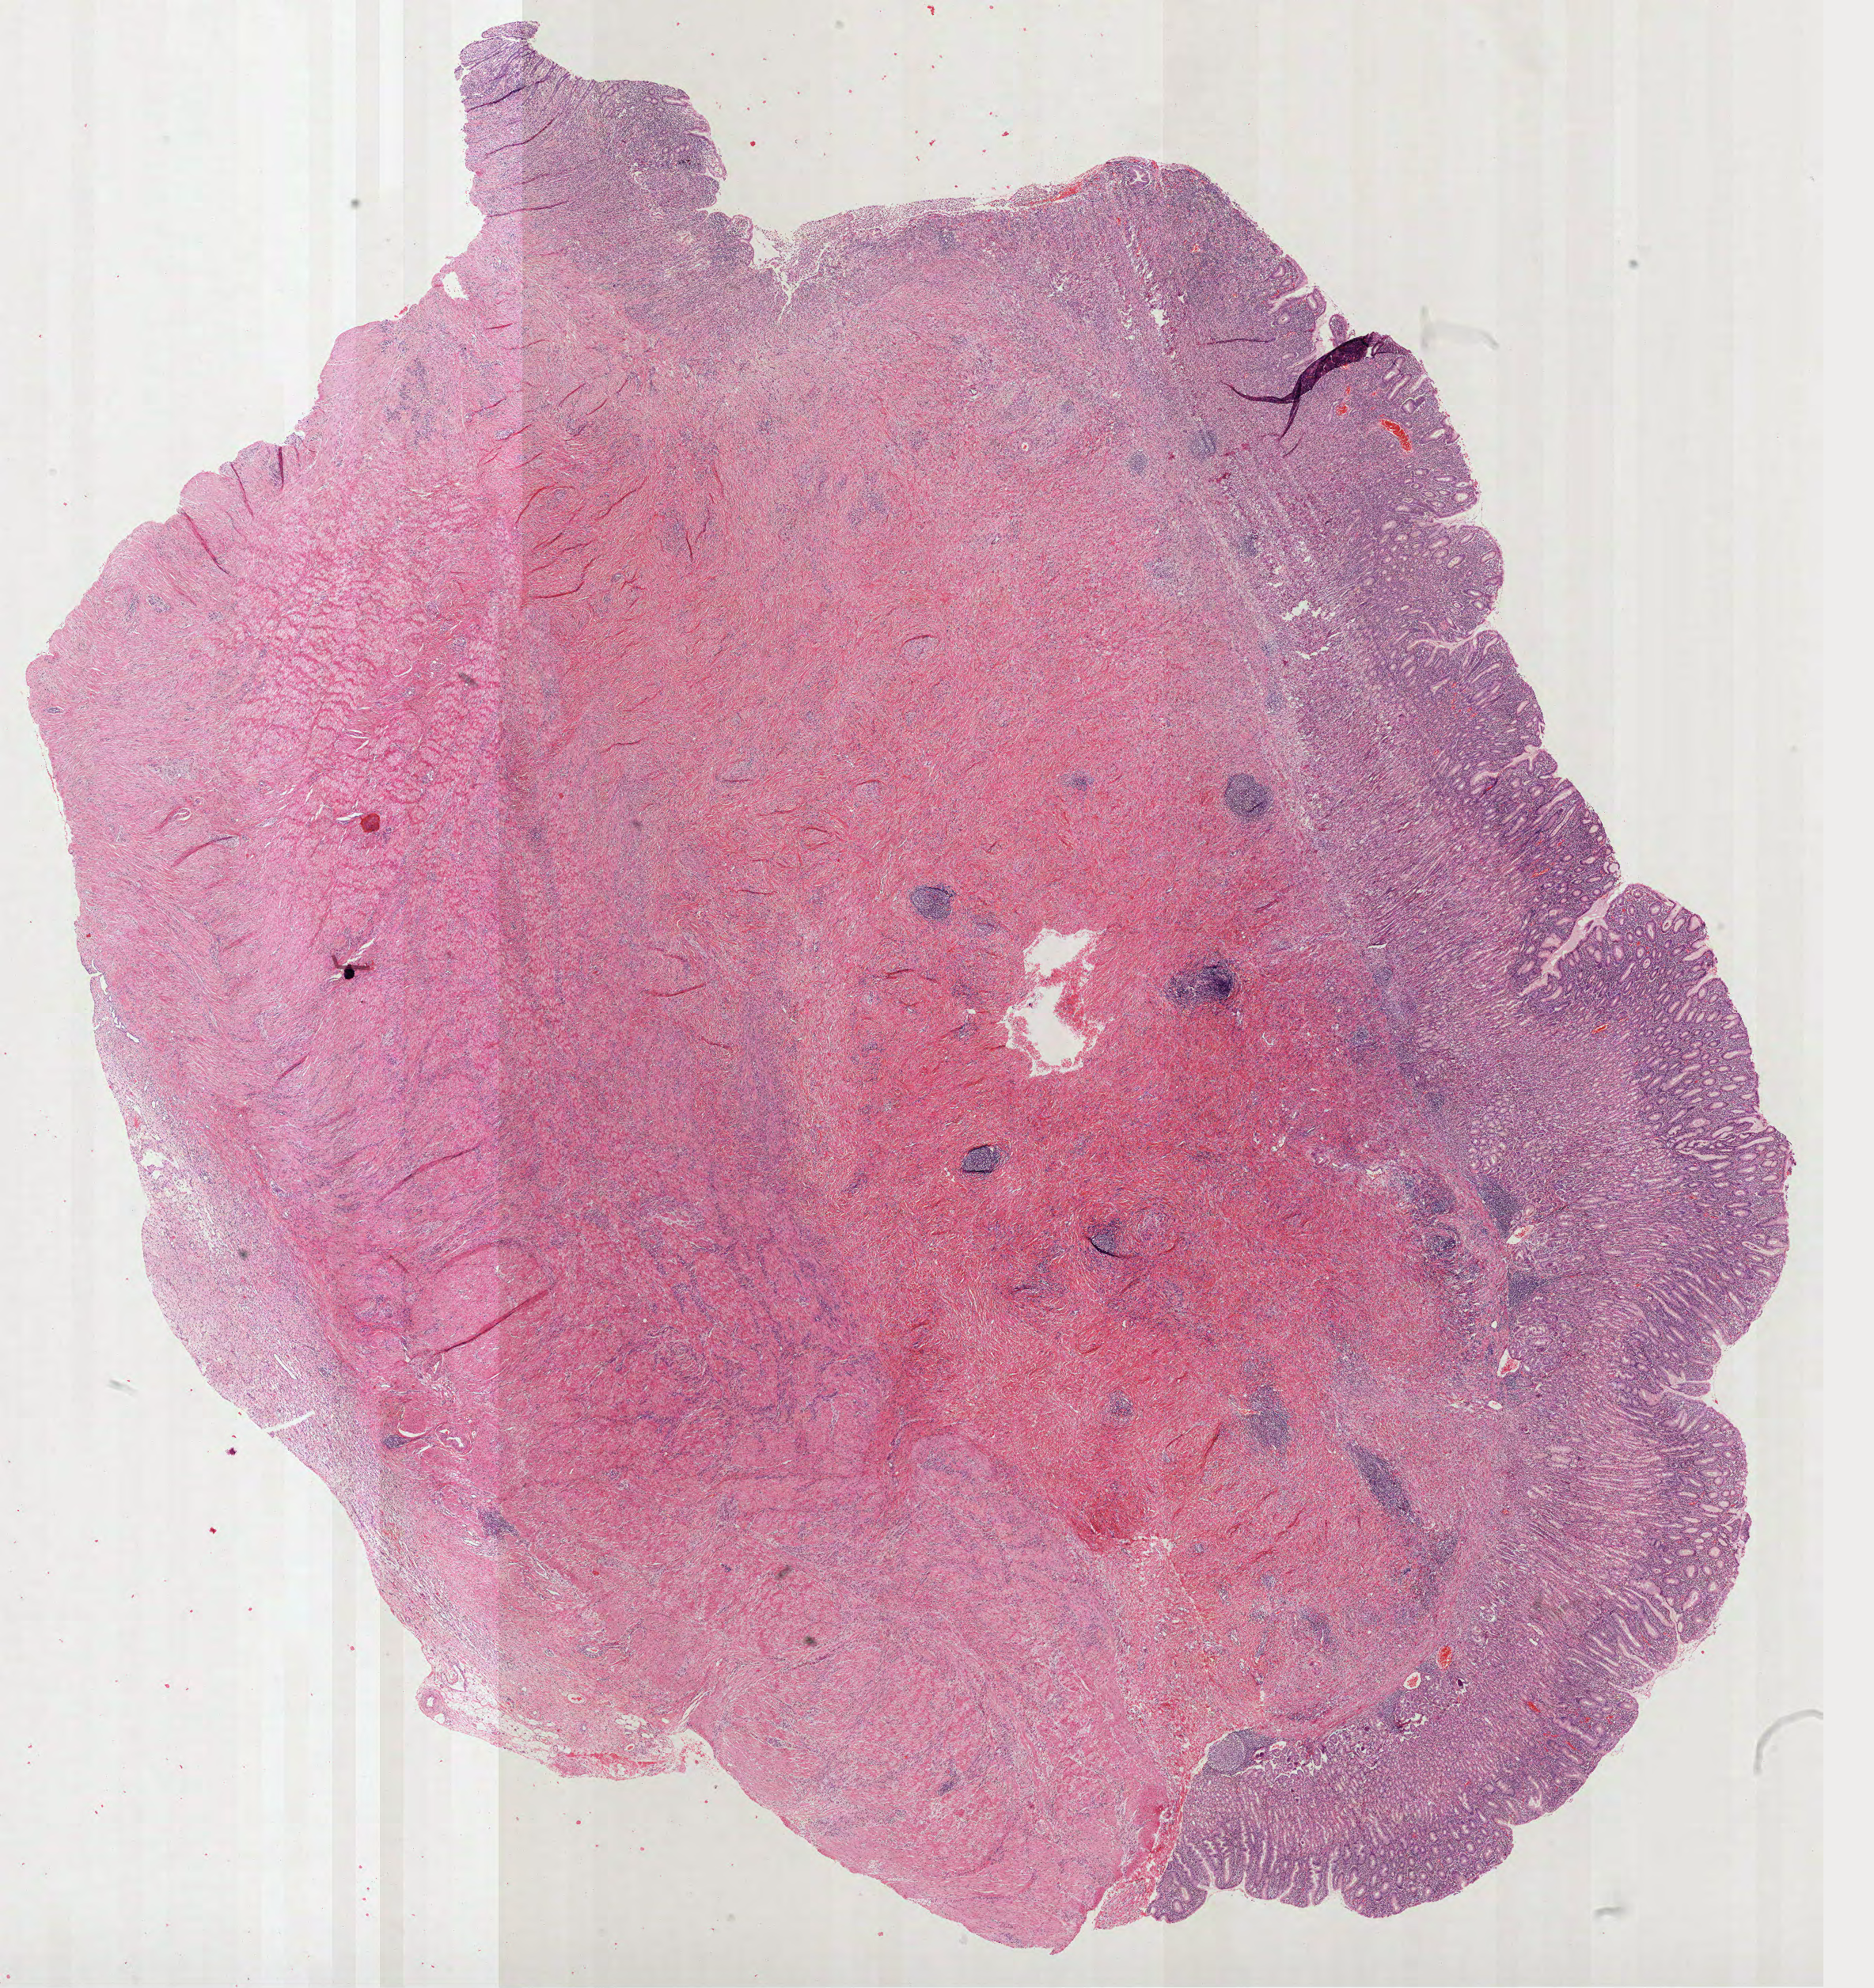
Whole-slide histology image, H&E — whole scanned area (about 19.1 x 20.3 mm) shown as a low-resolution overview; FFPE section; primary tumour sample from the stomach. Female patient; age at initial diagnosis 42 years.
Histologic diagnosis: Carcinoma, diffuse type (fundus of stomach).